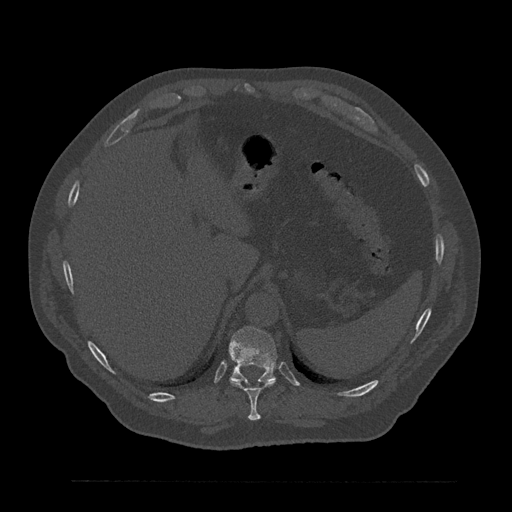
CT including the spine, one axial slice. Position 322 of 797 along the scan axis. Reconstruction kernel Br40s/3. Bone window (W 1800 / L 400 HU). 0.5 mm slice thickness. 512 × 512 image matrix, field of view 430 × 430 mm. Male patient, age 61 years. Case-level facts recorded for this patient, not image findings: primary cancer: prostate.
Outlined on this slice (semi-automatically segmented with operator editing):
- T10 vertebra: box from (x=229, y=379) to (x=276, y=421) px
- T11 vertebra: (x=230, y=326)–(x=277, y=384)